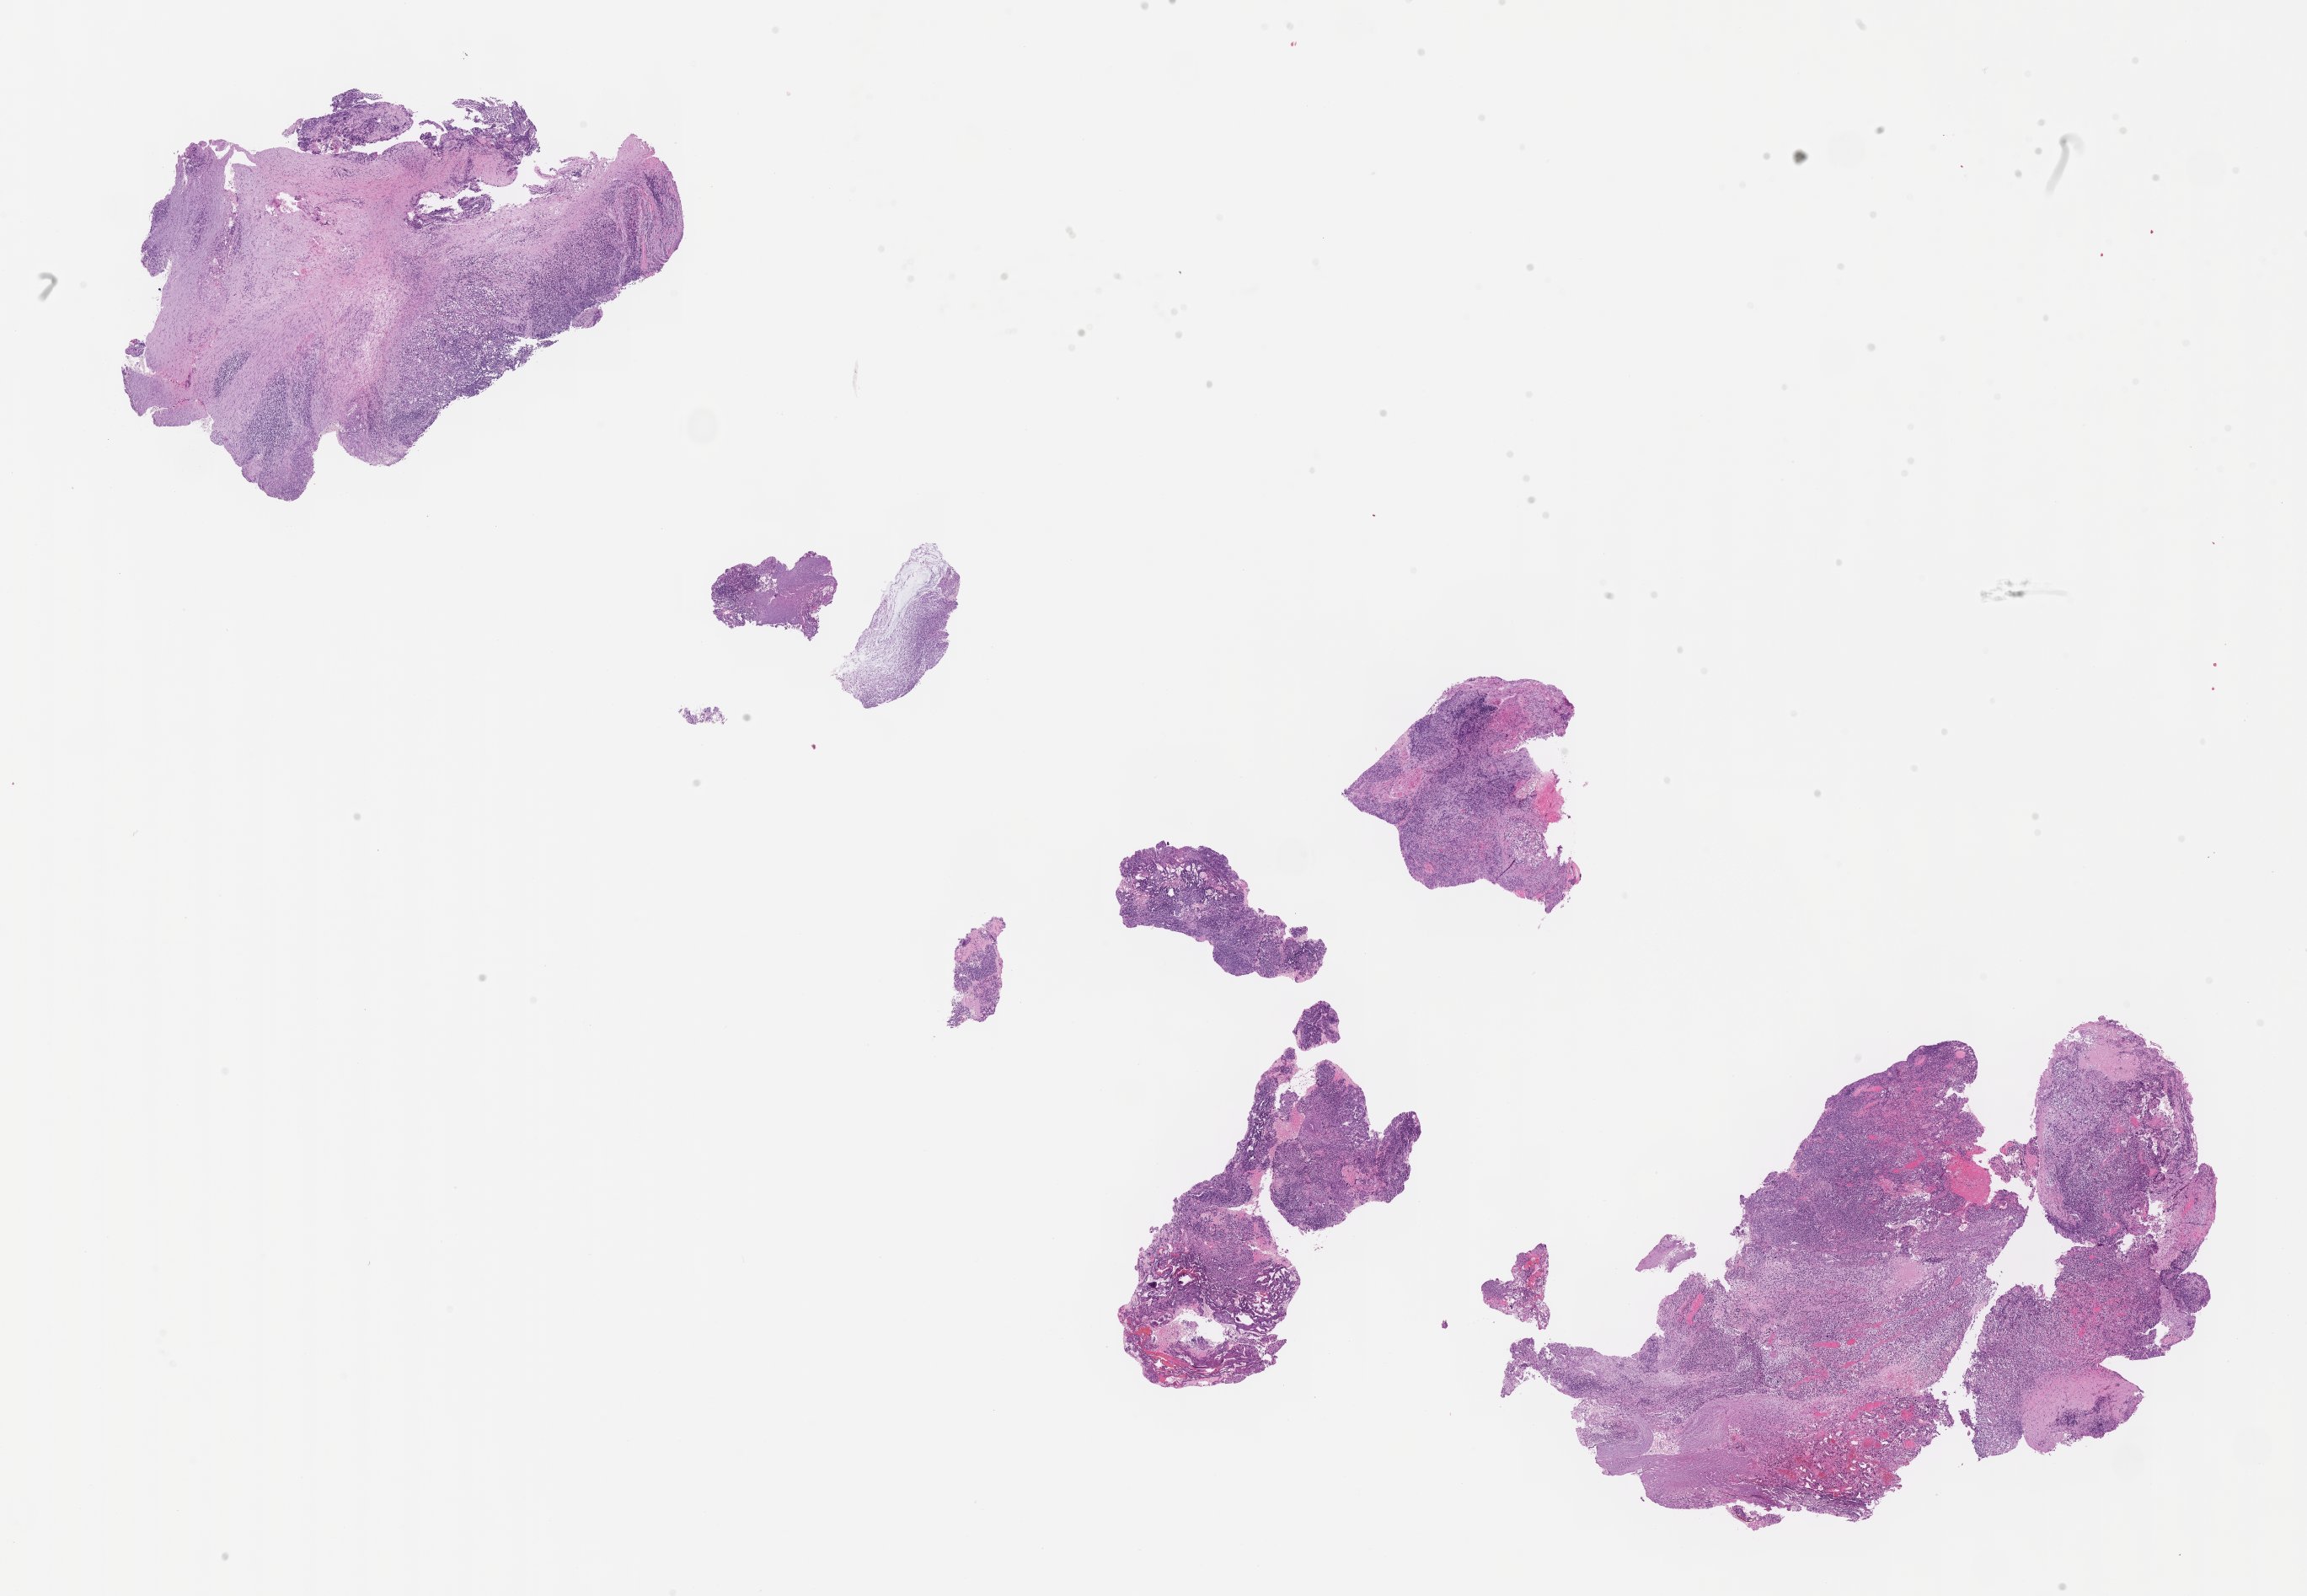
Whole-slide image, H&E stain of tumor tissue — whole scanned area (about 22.1 x 15.3 mm) shown as a low-resolution overview, FFPE section, site: tonsil-right. Male patient, age at diagnosis 3.8 years.
Stage (as recorded): 2. Metastatic status at presentation (as recorded): non-metastatic. Diagnosis: rhabdomyosarcoma; histological classification: embryonal rhabdomyosarcoma.